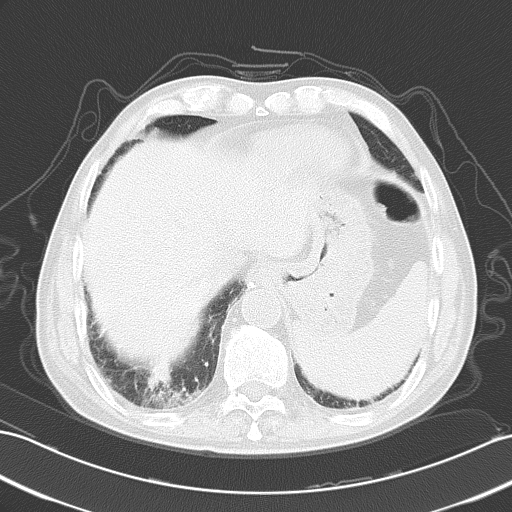
Chest CT, one axial slice. Slice 11 of 51 in the series (ordered by position). Lung window (W 1500 / L -600 HU). 5 mm slice thickness. 512 × 512 image matrix, field of view 353 × 353 mm. Patient: male, 73 years. From the clinical record (not read from this slice): clinical TNM (as recorded): T1a N0 M0; histopathological grade: G3.
Annotated regions visible in this slice (rectangle marked by the reading radiologist):
- lung tumour (recorded histology: small cell carcinoma): bounding box <138,365,178,399> (left, top, right, bottom; pixels)